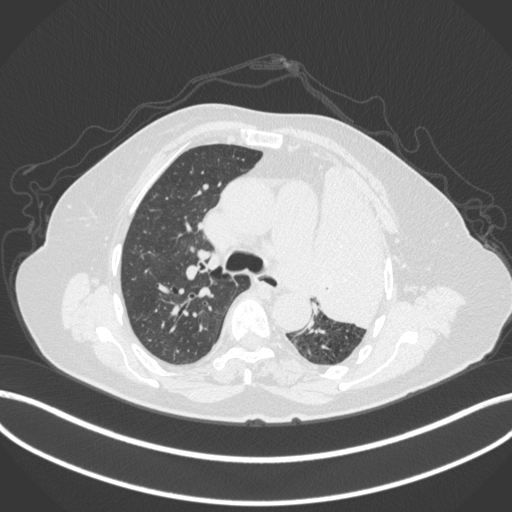
Chest CT, one axial slice. Position 257 of 399 along the scan axis. Reconstruction kernel B31f. 120 kVp. Lung window (W 1500 / L -600 HU). 512 × 512 image matrix, field of view 400 × 400 mm. Patient: female, 75 years. From the clinical record (not read from this slice): clinical TNM (as recorded): T3 N3 M1.
Structures marked on this image (rectangle marked by the reading radiologist):
- lung tumour (recorded histology: adenocarcinoma): bounding box [x1, y1, x2, y2] px = [316, 149, 395, 331]